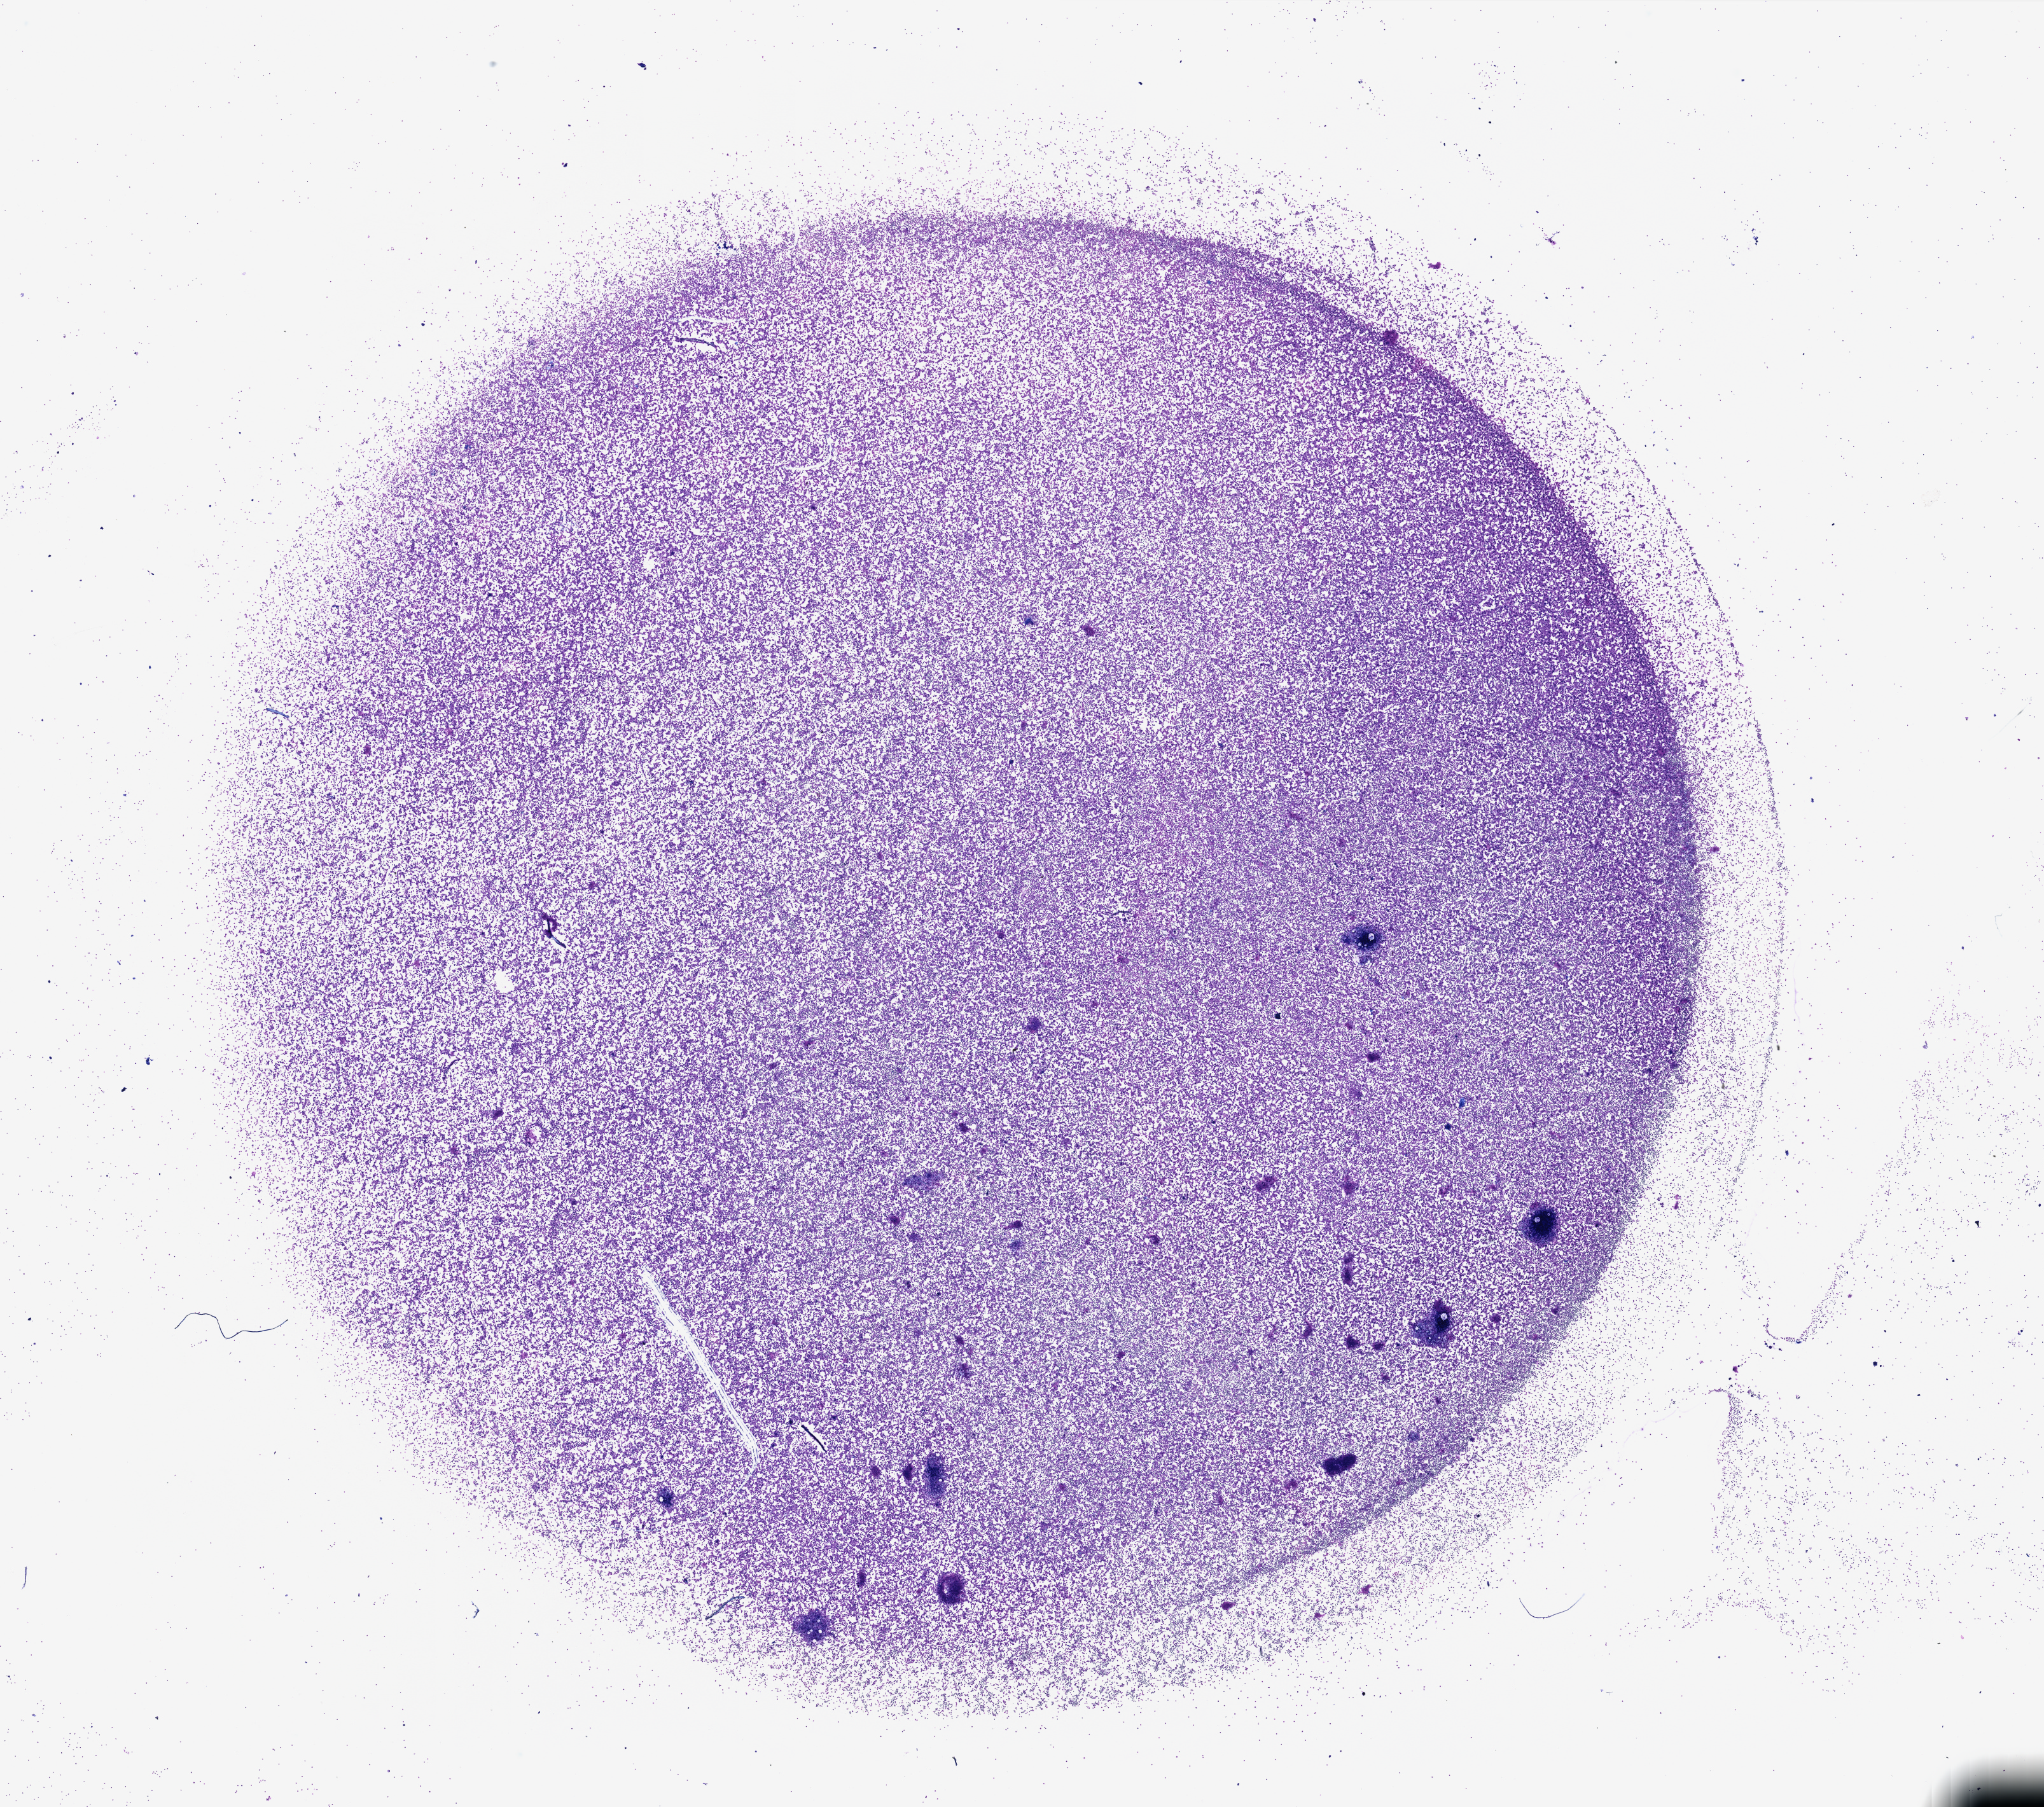
Hematoxylin and eosin (H&E) stained whole-slide image, whole scanned area (about 25.4 x 22.4 mm, acquisition: 40x scan) shown as a low-resolution overview, bone marrow (leukaemic) sample. 55-year-old female patient. Blasts: 30%.
- WHO classification: AML with maturation
- diagnosis: Acute Myeloid Leukemia
- FAB classification: M2